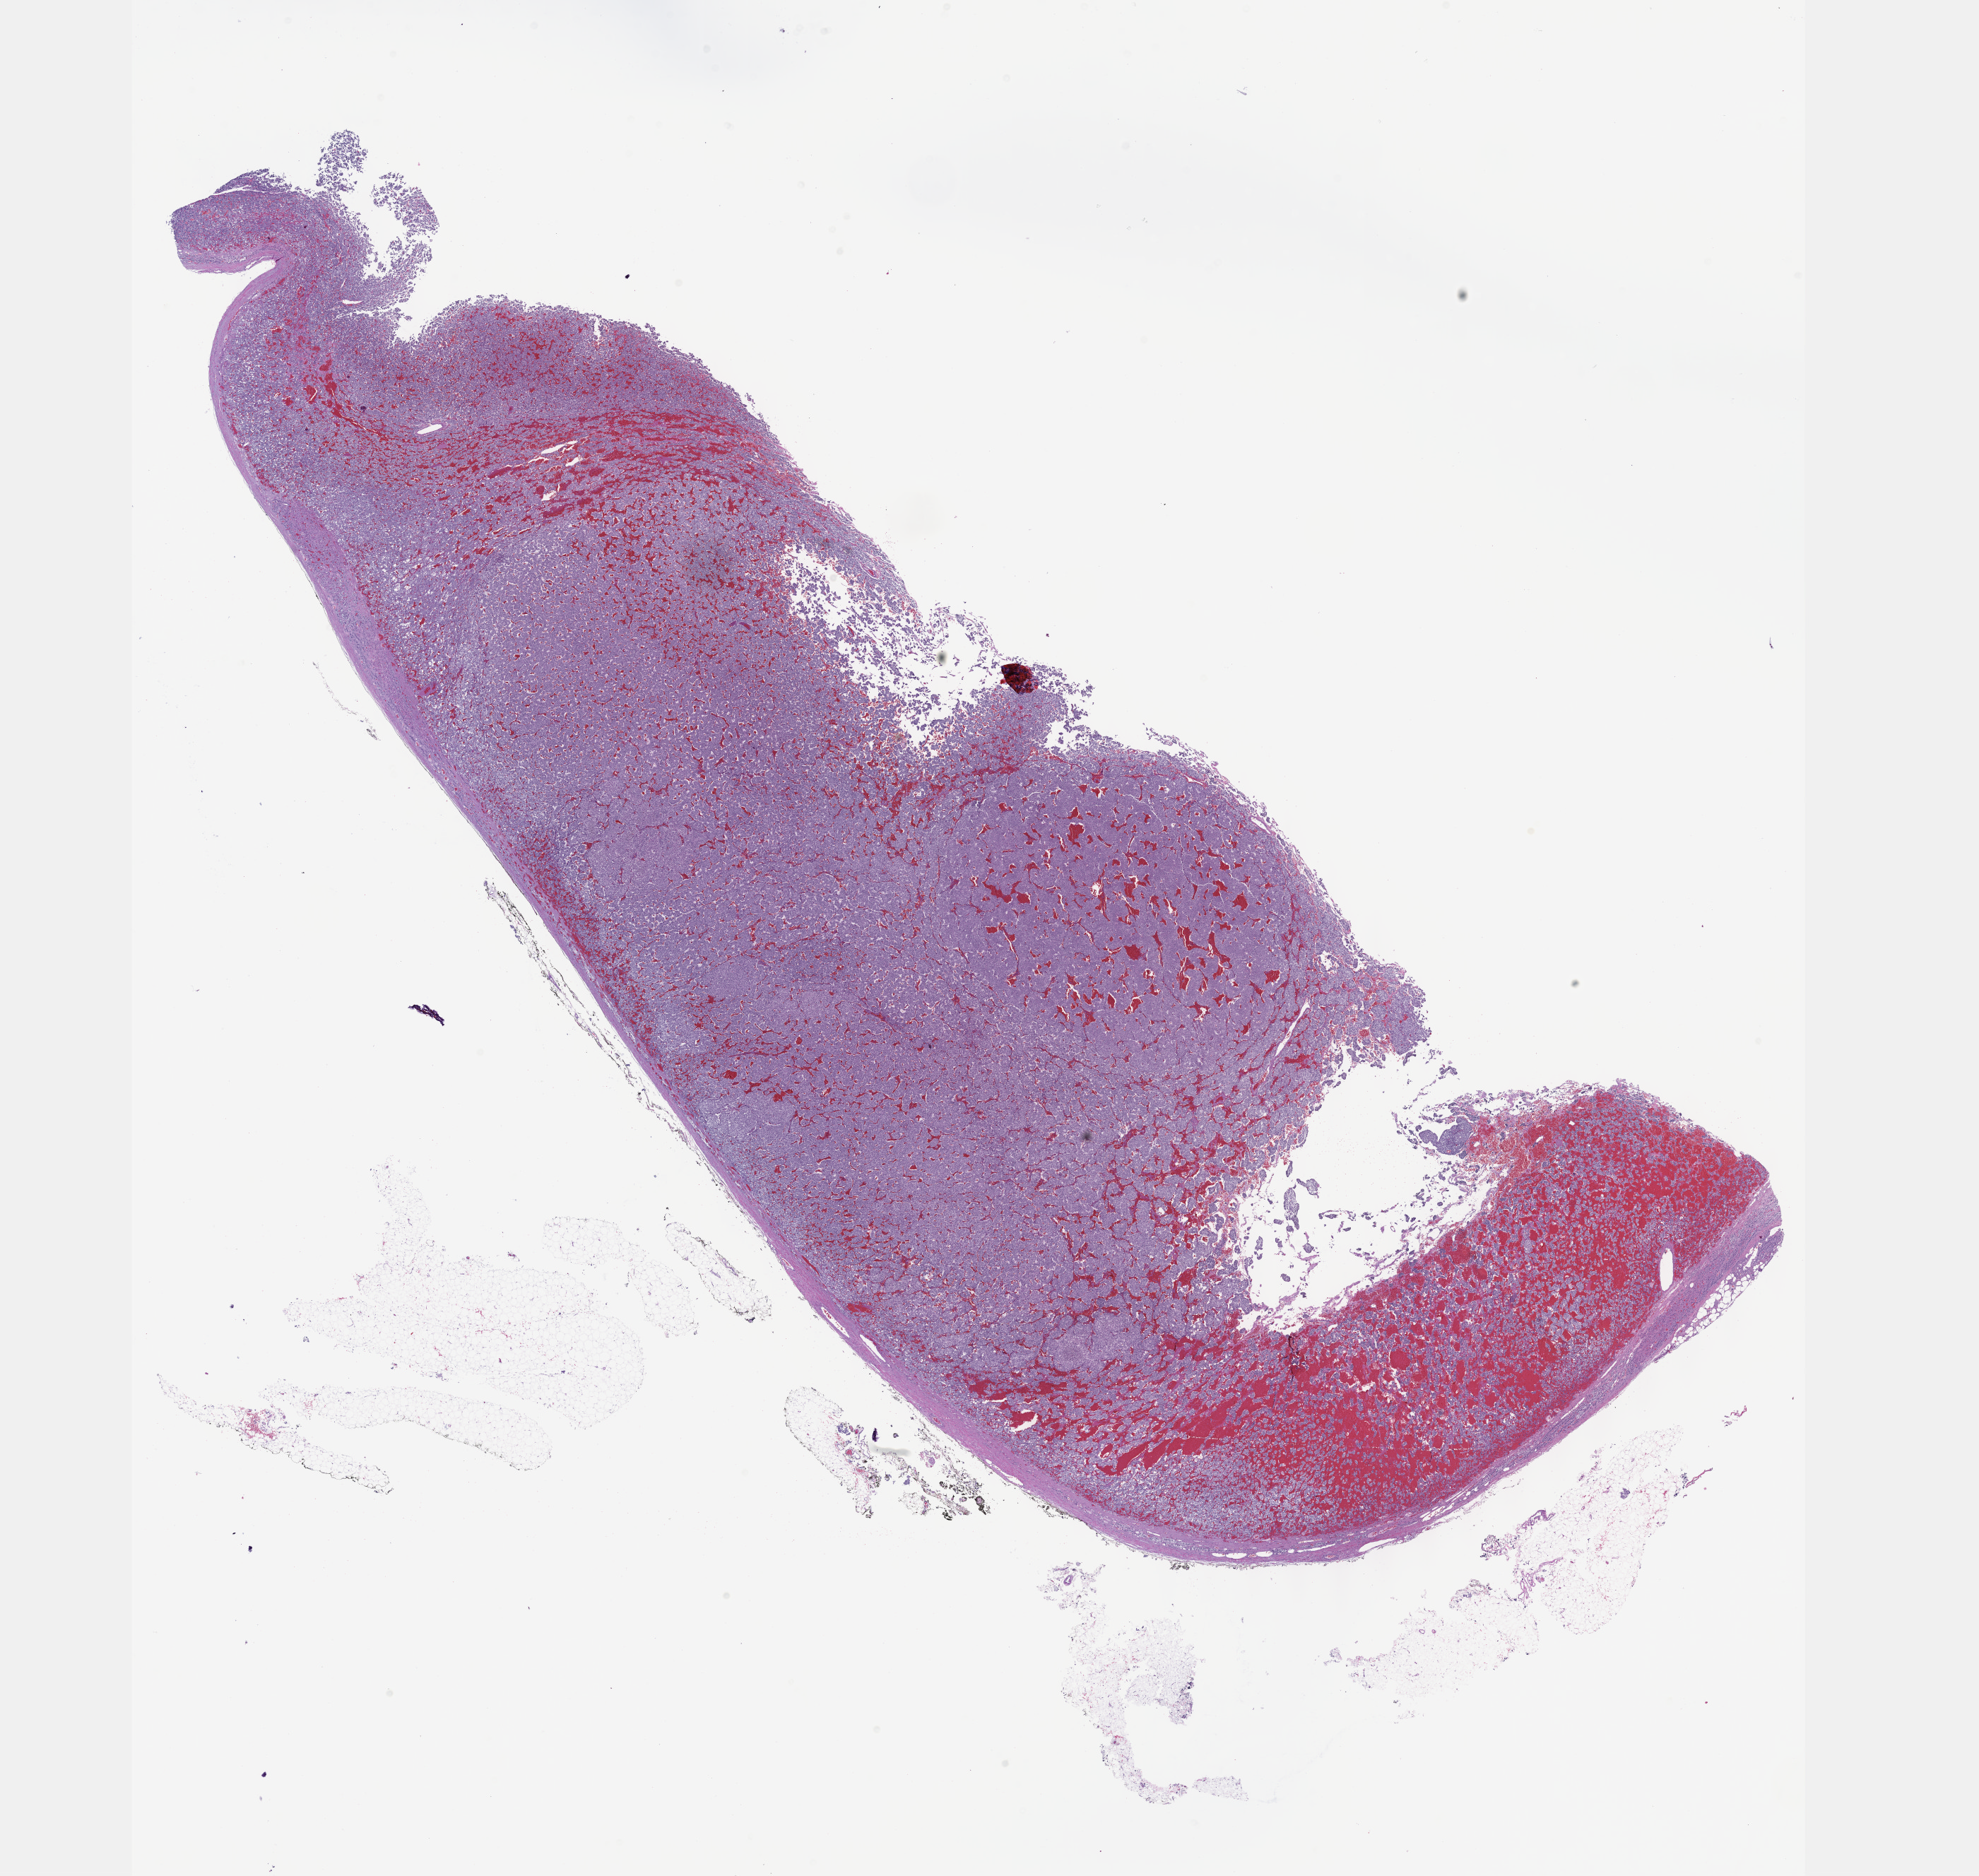
Hematoxylin and eosin (H&E) stained whole-slide image, whole scanned area (about 22.6 x 21.5 mm) shown as a low-resolution overview. FFPE section. Adrenal gland, primary tumour sample. Female, age 35 years at initial diagnosis.
Pathologic diagnosis: Pheochromocytoma, NOS. Laterality: left.